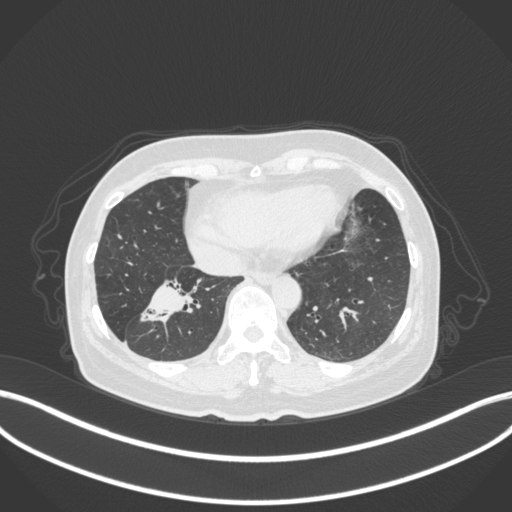
Chest CT, one axial slice; slice 120 of 429 in the series (ordered by position); lung window (W 1500 / L -600 HU); 512 × 512 image matrix. Female patient, age 67 years. Case-level facts recorded for this patient, not image findings: clinical TNM (as recorded): T1c N1 M0.
Structures marked on this image (bounding box drawn by a radiologist):
- lung tumour (recorded histology: adenocarcinoma): bounding box [x1, y1, x2, y2] px = [135, 270, 209, 329]